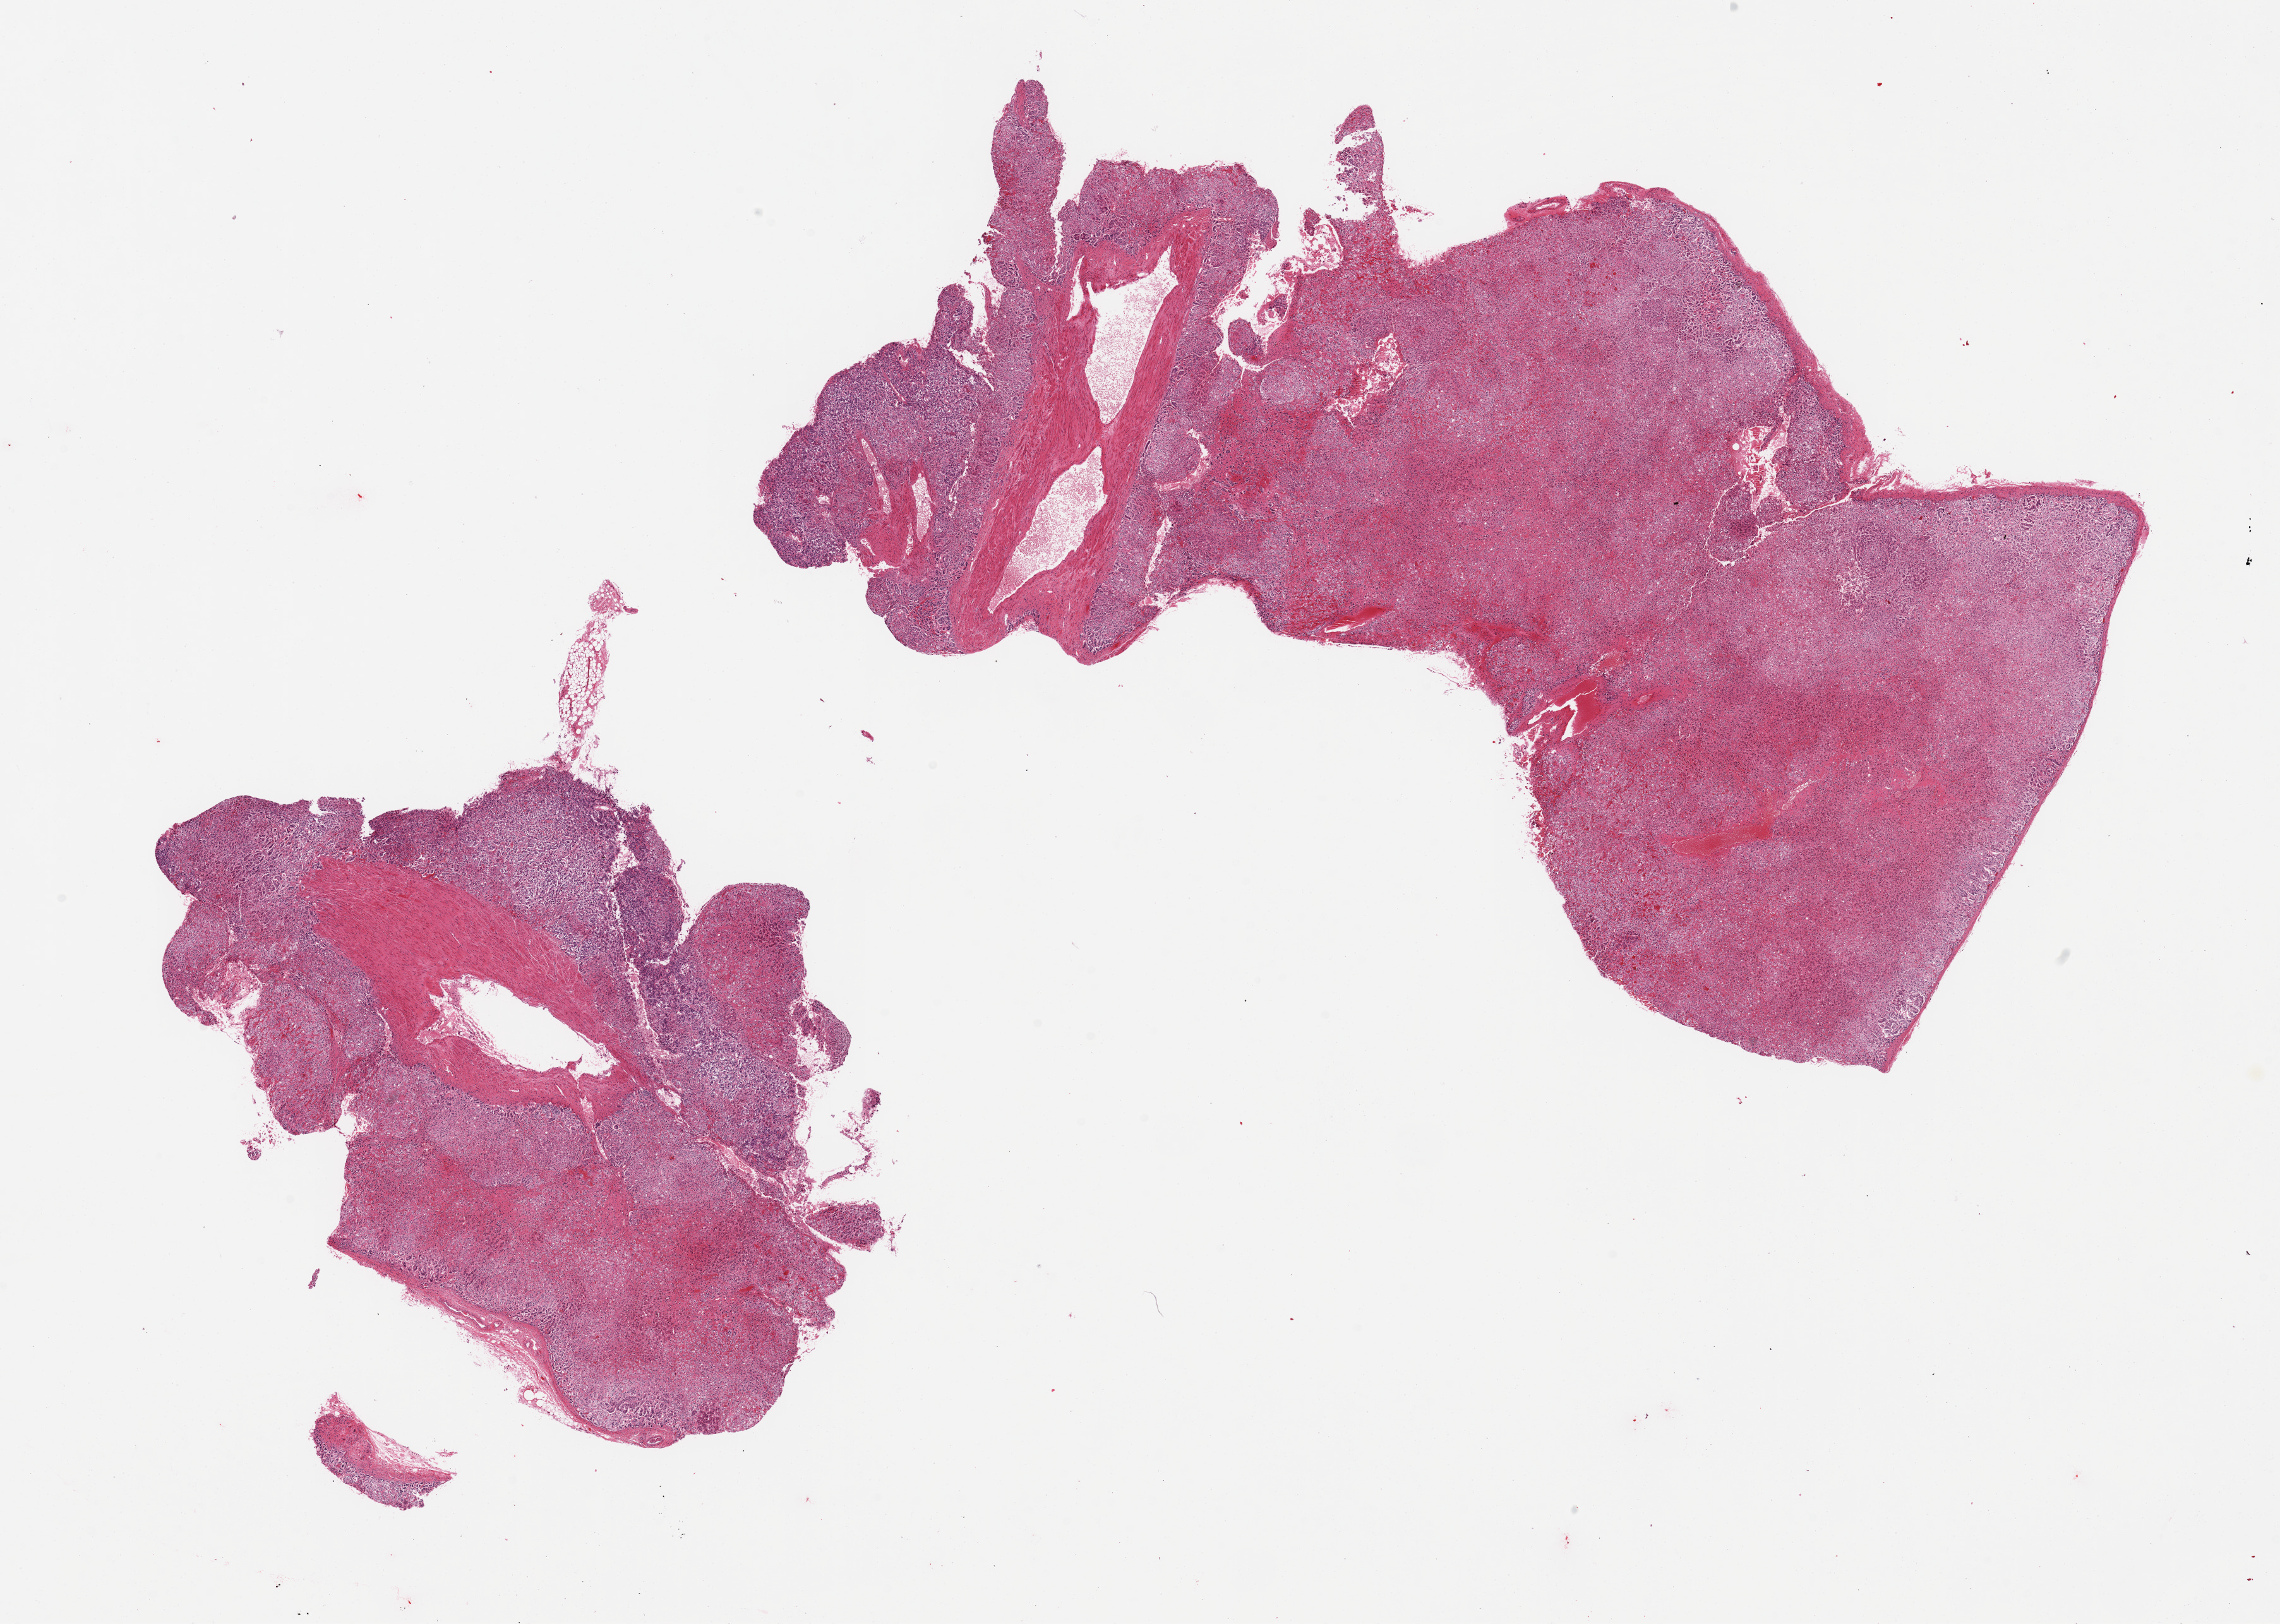
Whole-slide image, haematoxylin and eosin stain — low-resolution overview of the scanned area, about 28.5 x 20.3 mm (from a 20x scan). PAXgene-fixed paraffin-embedded (PFPE) section. Target tissue: adrenal gland. Donor tissue sample. Donor sex: female.
* pathologist's review note for this sample: 2 pieces